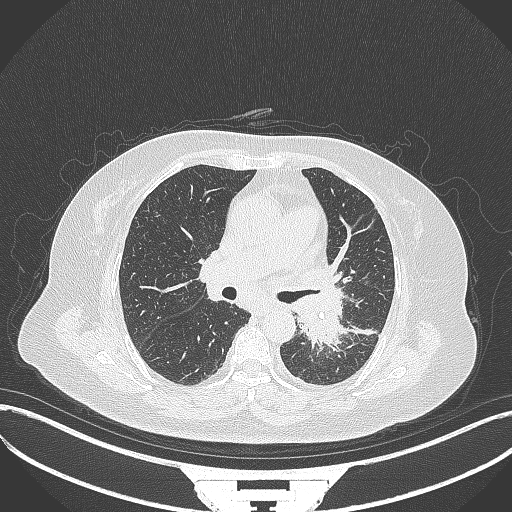
Chest CT, one axial slice. Slice 201 of 322 in the series (ordered by position). 120 kVp. Lung window (W 1500 / L -600 HU). 1 mm slice thickness. 512 × 512 image matrix, field of view 400 × 400 mm. Patient: female, 69 years. Case-level facts recorded for this patient, not image findings: clinical TNM (as recorded): T2b N3 M1.
Structures marked on this image (rectangle marked by the reading radiologist):
- lung tumour (recorded histology: adenocarcinoma): bounding box (x1, y1, x2, y2) in pixels: (287, 285, 345, 352)